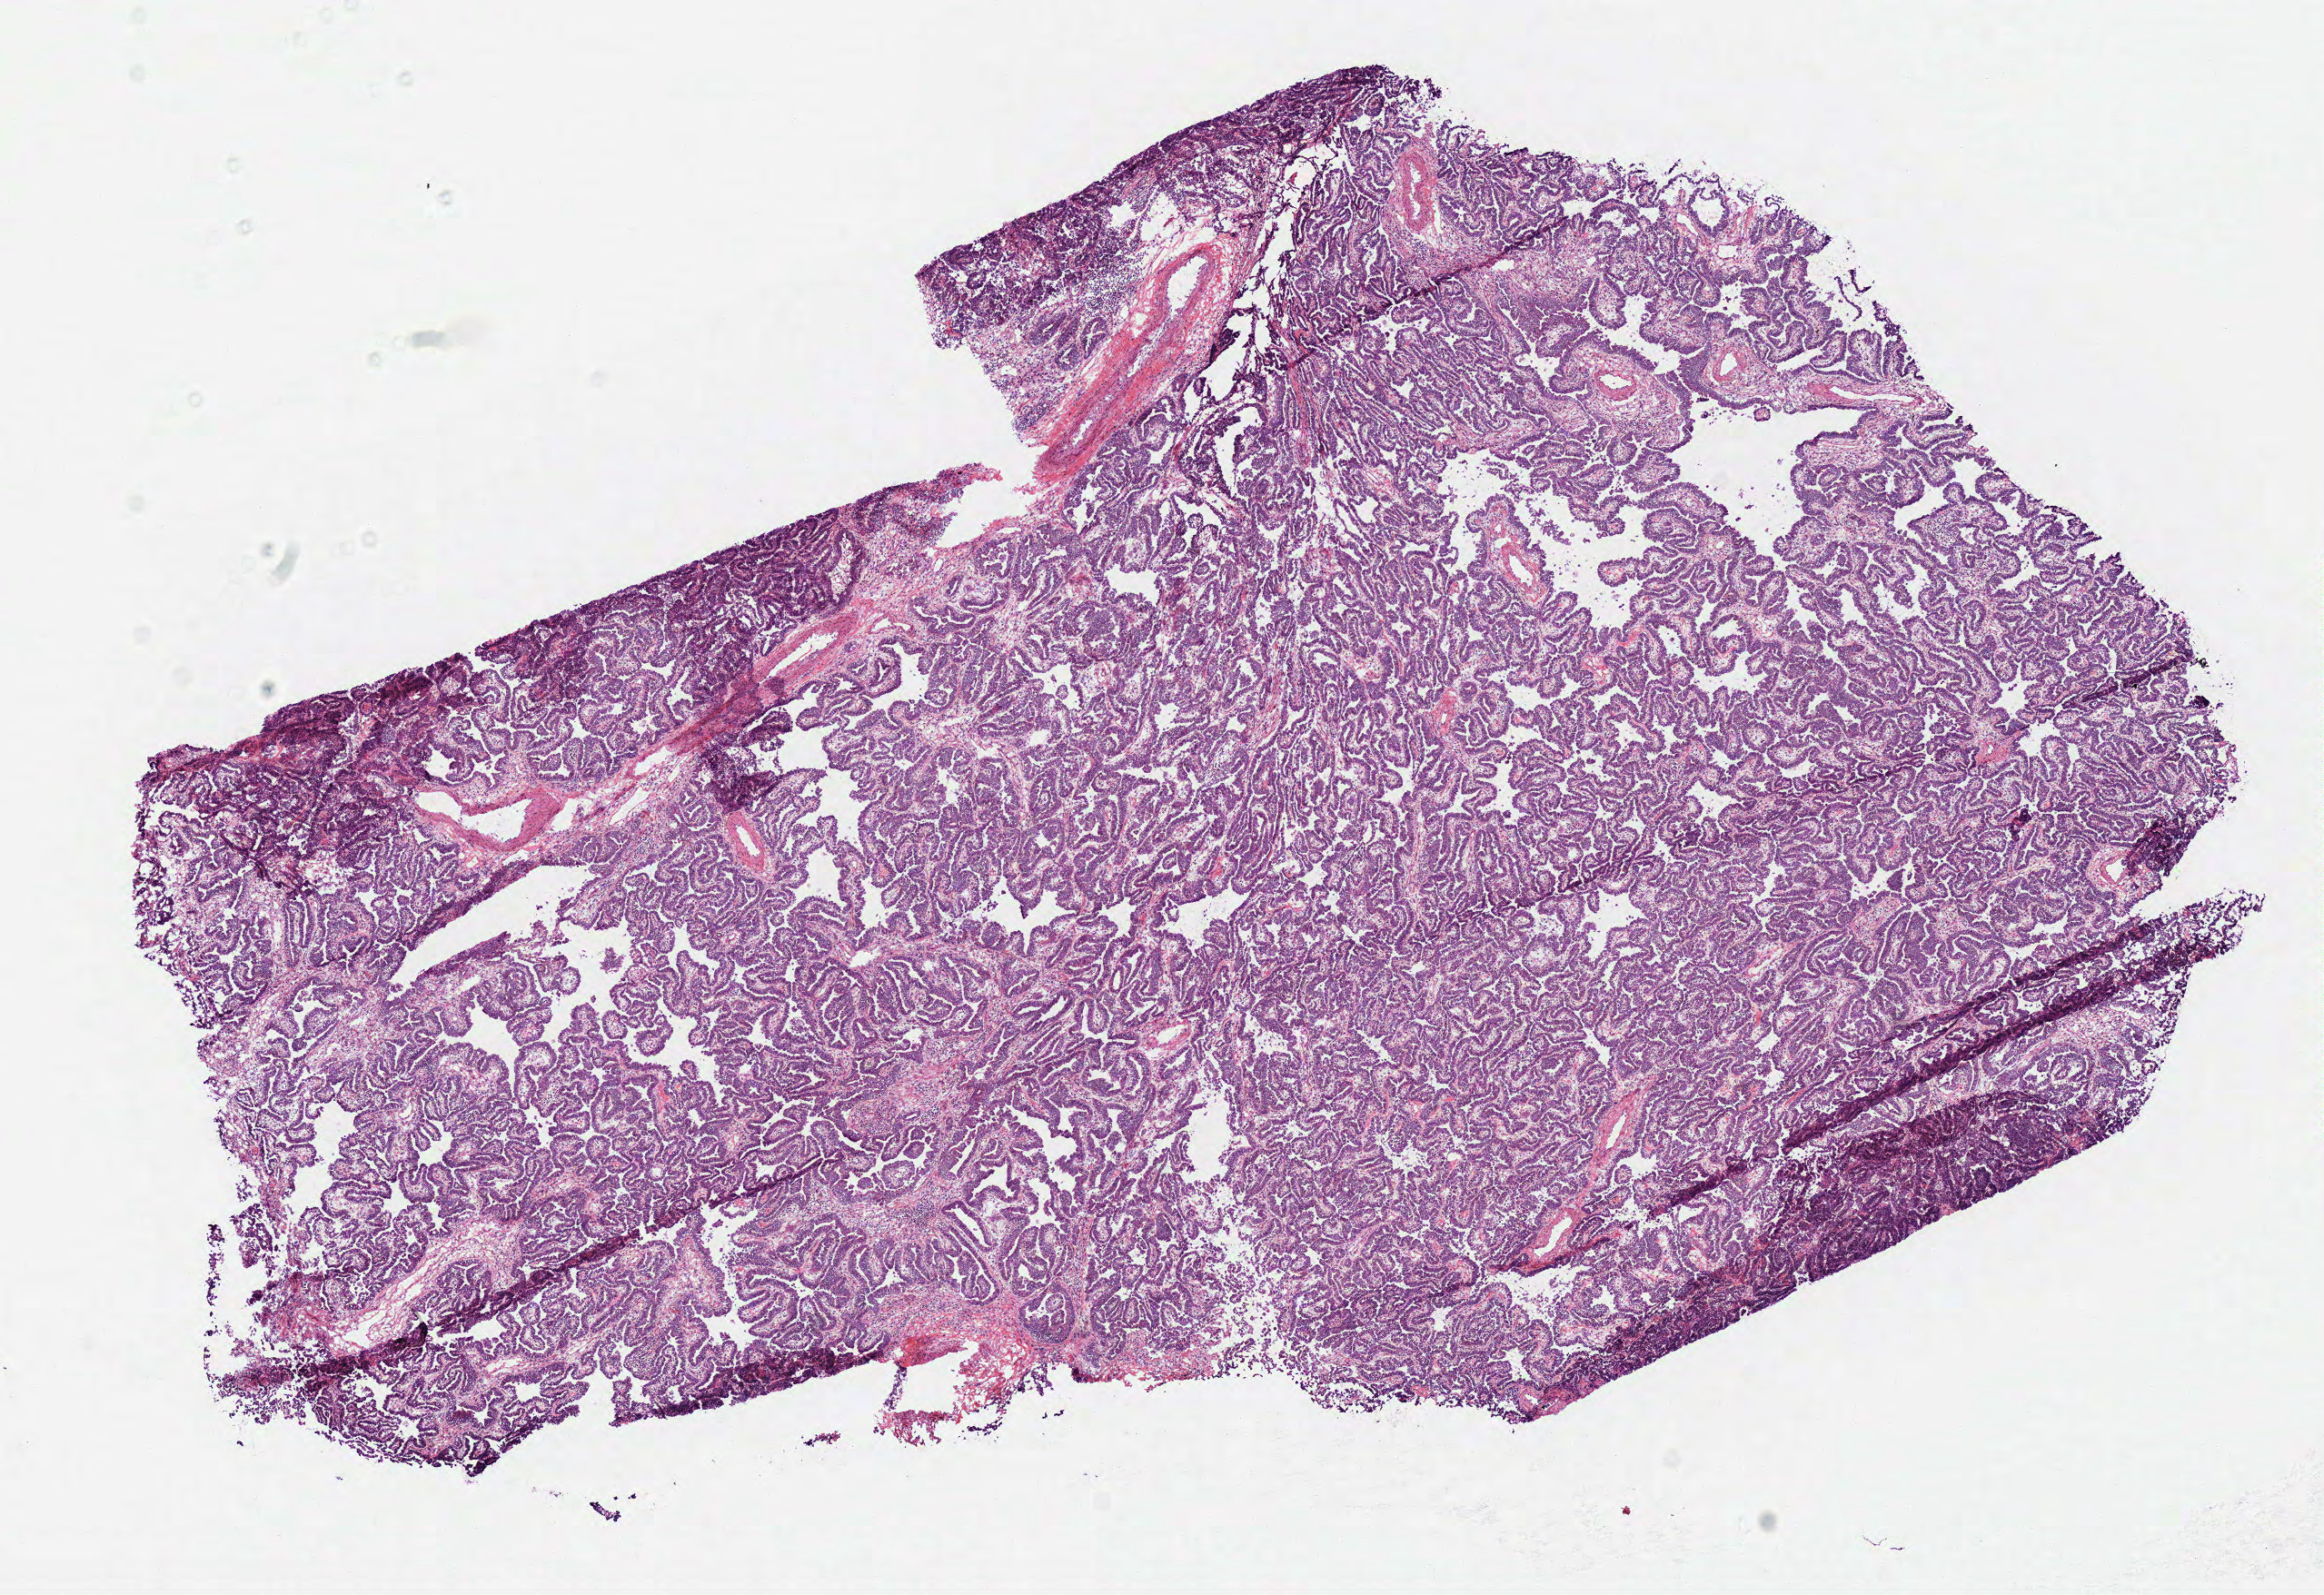
Digitized Hematoxylin and eosin (H&E) stained tissue section (whole slide), whole scanned area (about 10.1 x 6.9 mm) shown as a low-resolution overview, frozen section, sample: primary tumour, lung. Male patient; age at initial diagnosis 77 years. Composition of this section per pathologist review: tumour cells 85%, tumour nuclei 75%, normal cells 0%, stromal cells 15%, necrosis 0%.
Pathologic diagnosis: Papillary adenocarcinoma, NOS. AJCC pathologic stage: IV (6th edition).